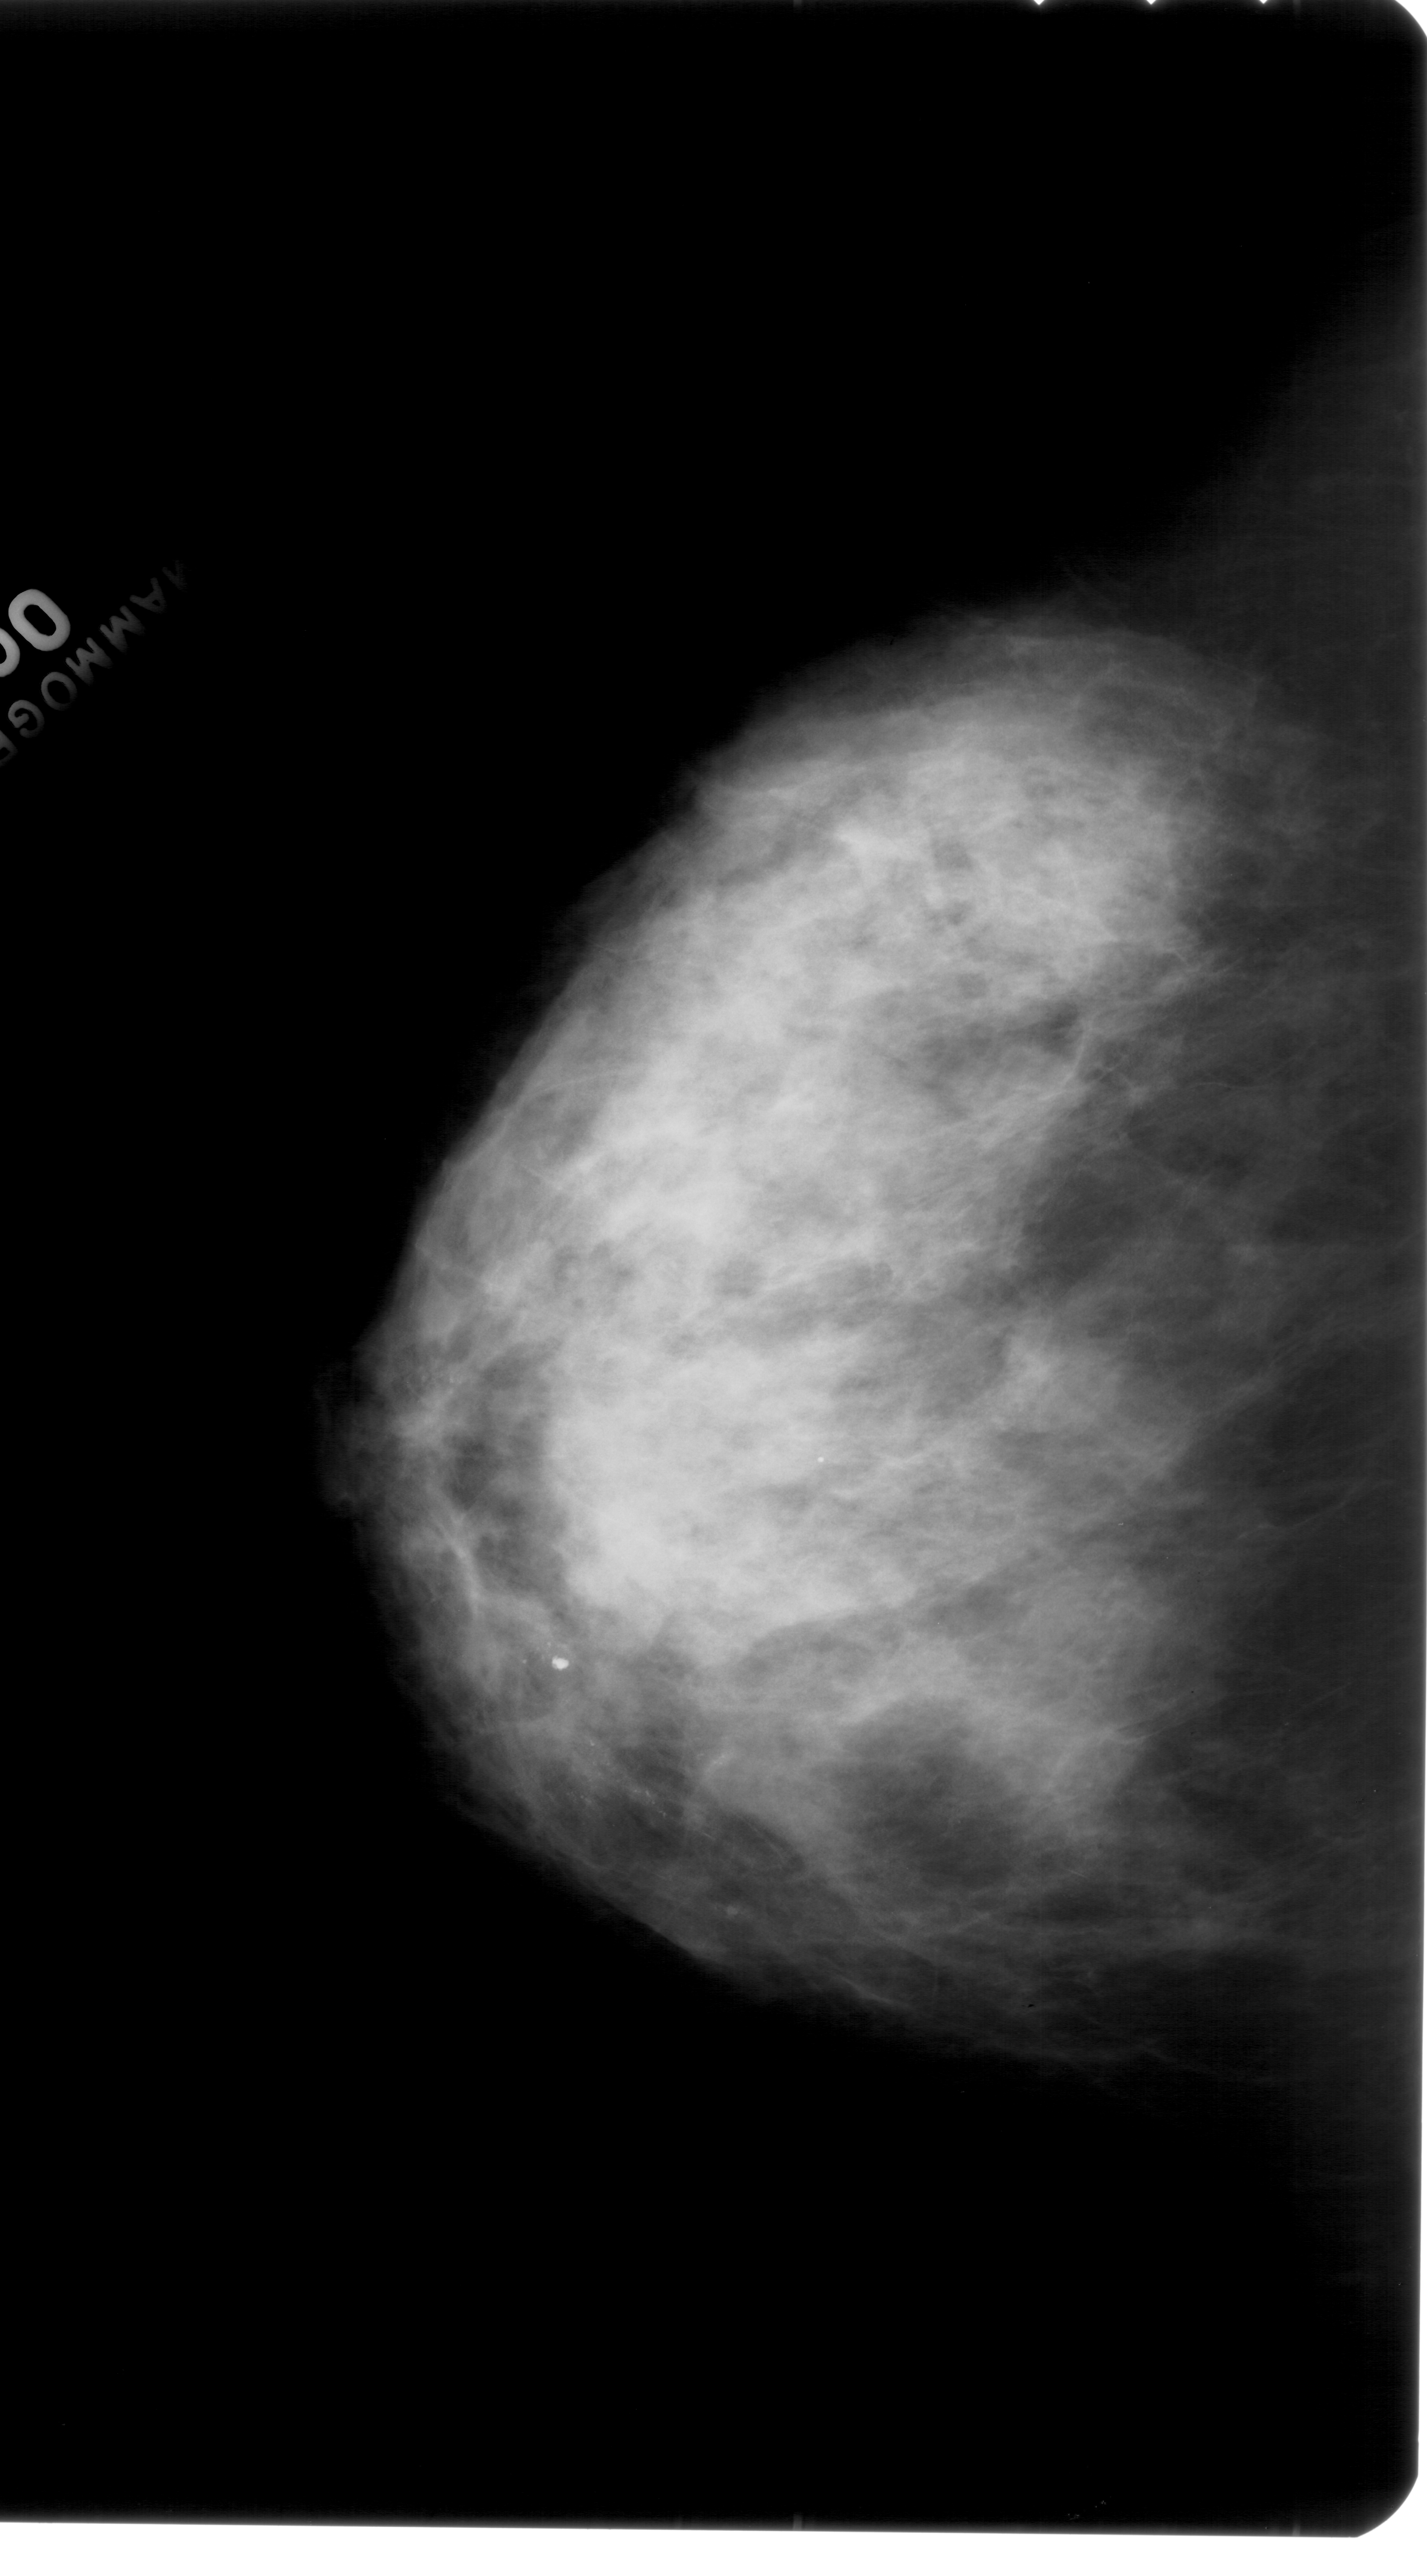
Mammogram (digitized film); left breast; CC view; BI-RADS breast density category 4 (scale 1–4); 1427 × 2576 image matrix.
Expert-marked regions of interest on this image (one box per marked abnormality):
- calcifications, morphology pleomorphic, distribution linear; BI-RADS assessment category 4; subtlety rating 1 on a 1 (subtle) to 5 (obvious) scale; pathology result (as recorded, not read from the image): malignant: bounding box <572,1720,764,1854> (left, top, right, bottom; pixels)